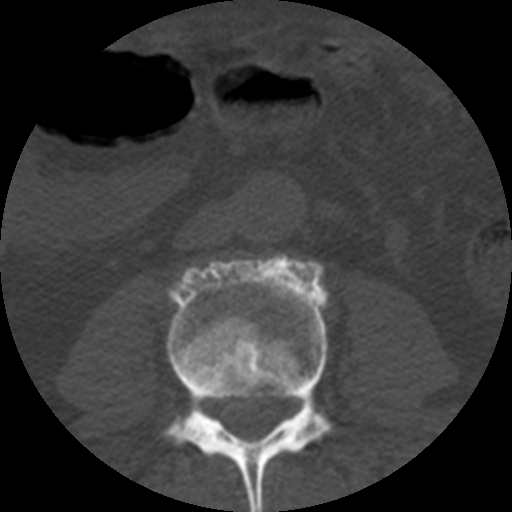
CT including the spine, one axial slice; position 118 of 508 along the scan axis; reconstruction kernel STANDARD; 120 kVp; bone window (W 1800 / L 400 HU); 1.25 mm slice thickness; 512 × 512 image matrix. Patient age 57 years. Case-level facts recorded for this patient, not image findings: primary cancer: prostate.
Structures marked on this image (semi-automatically segmented with operator editing):
- L3 vertebra: bounding box [x1, y1, x2, y2] px = [162, 255, 333, 512]